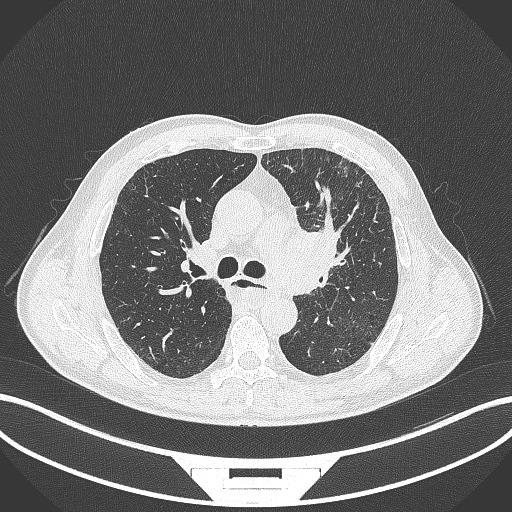
Chest CT, one axial slice; position 244 of 411 along the scan axis; lung window (W 1500 / L -600 HU); 512 × 512 image matrix, field of view 400 × 400 mm. Male patient, age 57 years. Case-level facts recorded for this patient, not image findings: clinical TNM (as recorded): T2a N1 M0.
Annotated regions visible in this slice (rectangle marked by the reading radiologist):
- lung tumour (recorded histology: squamous cell carcinoma): bounding box [x1, y1, x2, y2] px = [274, 221, 361, 303]